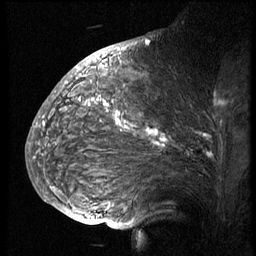
Breast MRI (dynamic contrast-enhanced), one sagittal slice; slice 40 of 74 in the series (ordered by position); 3 images stored at this slice position (order not interpretable as contrast timing); 1.5 T; TE 4.2 ms, TR 8.9 ms; 2.5 mm slice thickness; 256 × 256 image matrix. Patient: female, 57 years. Case-level facts recorded for this patient, not image findings: setting: breast cancer imaged before/during neoadjuvant chemotherapy; receptor status: HER2-positive.
Structures marked on this image (semi-automatic segmentation, software-assisted and operator-edited):
- analysis volume of interest (the breast-tissue region the enhancement analysis was run in; not a lesion): box from (x=51, y=67) to (x=248, y=173) px
- tumour enhancement mask (voxels above the 140 % enhancement threshold inside the analysis volume of interest): (x=92, y=99)–(x=168, y=147)